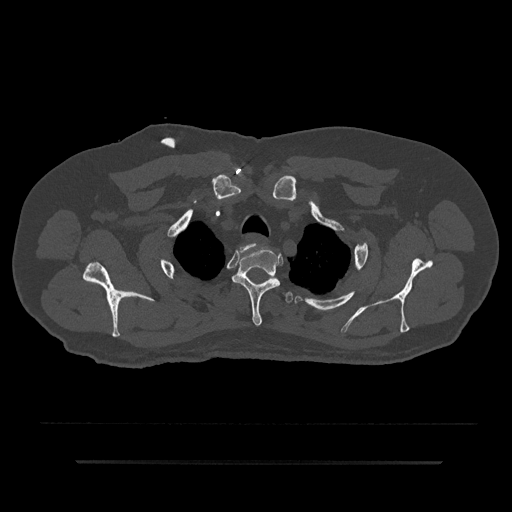
CT including the spine, one axial slice. Slice 695 of 797 in the series (ordered by position). 120 kVp. Bone window (W 1800 / L 400 HU). 0.5 mm slice thickness. 512 × 512 image matrix, field of view 464 × 464 mm. Patient: male, 59 years. Case-level facts recorded for this patient, not image findings: primary cancer: bile ducts; vertebrae with lytic lesions (as recorded): T10.
Structures marked on this image (semi-automatic segmentation, software-assisted and operator-edited):
- T1 vertebra: bounding box (x1, y1, x2, y2) in pixels: (238, 244, 268, 264)
- T2 vertebra: (232, 250, 280, 326)
- T3 vertebra: (283, 292, 292, 304)